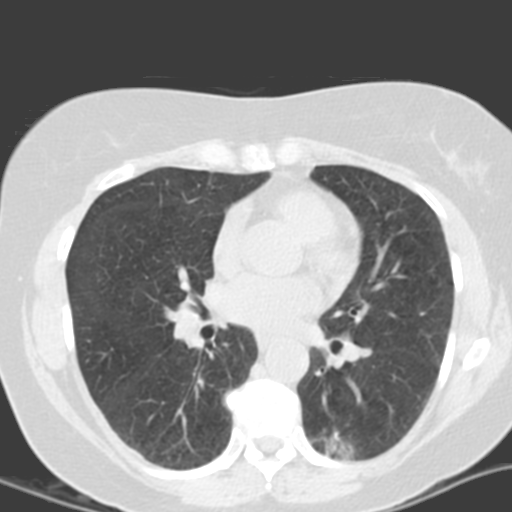
Chest CT (low-dose screening protocol), one axial image, second screening round (one year after baseline), lung window (W 1500 / L -600 HU), standard (soft-tissue) reconstruction kernel (B), 512 × 512 image matrix. Female participant, aged 55 years at enrolment. Current smoker at enrolment.
Expert-annotated lung lesion, bounding box (x1, y1, x2, y2) in pixels: (305, 410, 379, 467). The screening reader recorded 4 non-calcified nodules or masses ≥4 mm on this exam (left lower lobe, left lower lobe, left upper lobe, right middle lobe); which of them this box marks is not recorded. Official screen result: positive, other. Participant outcome: lung cancer diagnosed 688 days after this screen (after the third annual screen) — adenocarcinoma with mixed subtypes, left lower lobe, poorly differentiated (G3), stage IA (AJCC 6th edition), 21 mm at pathology.